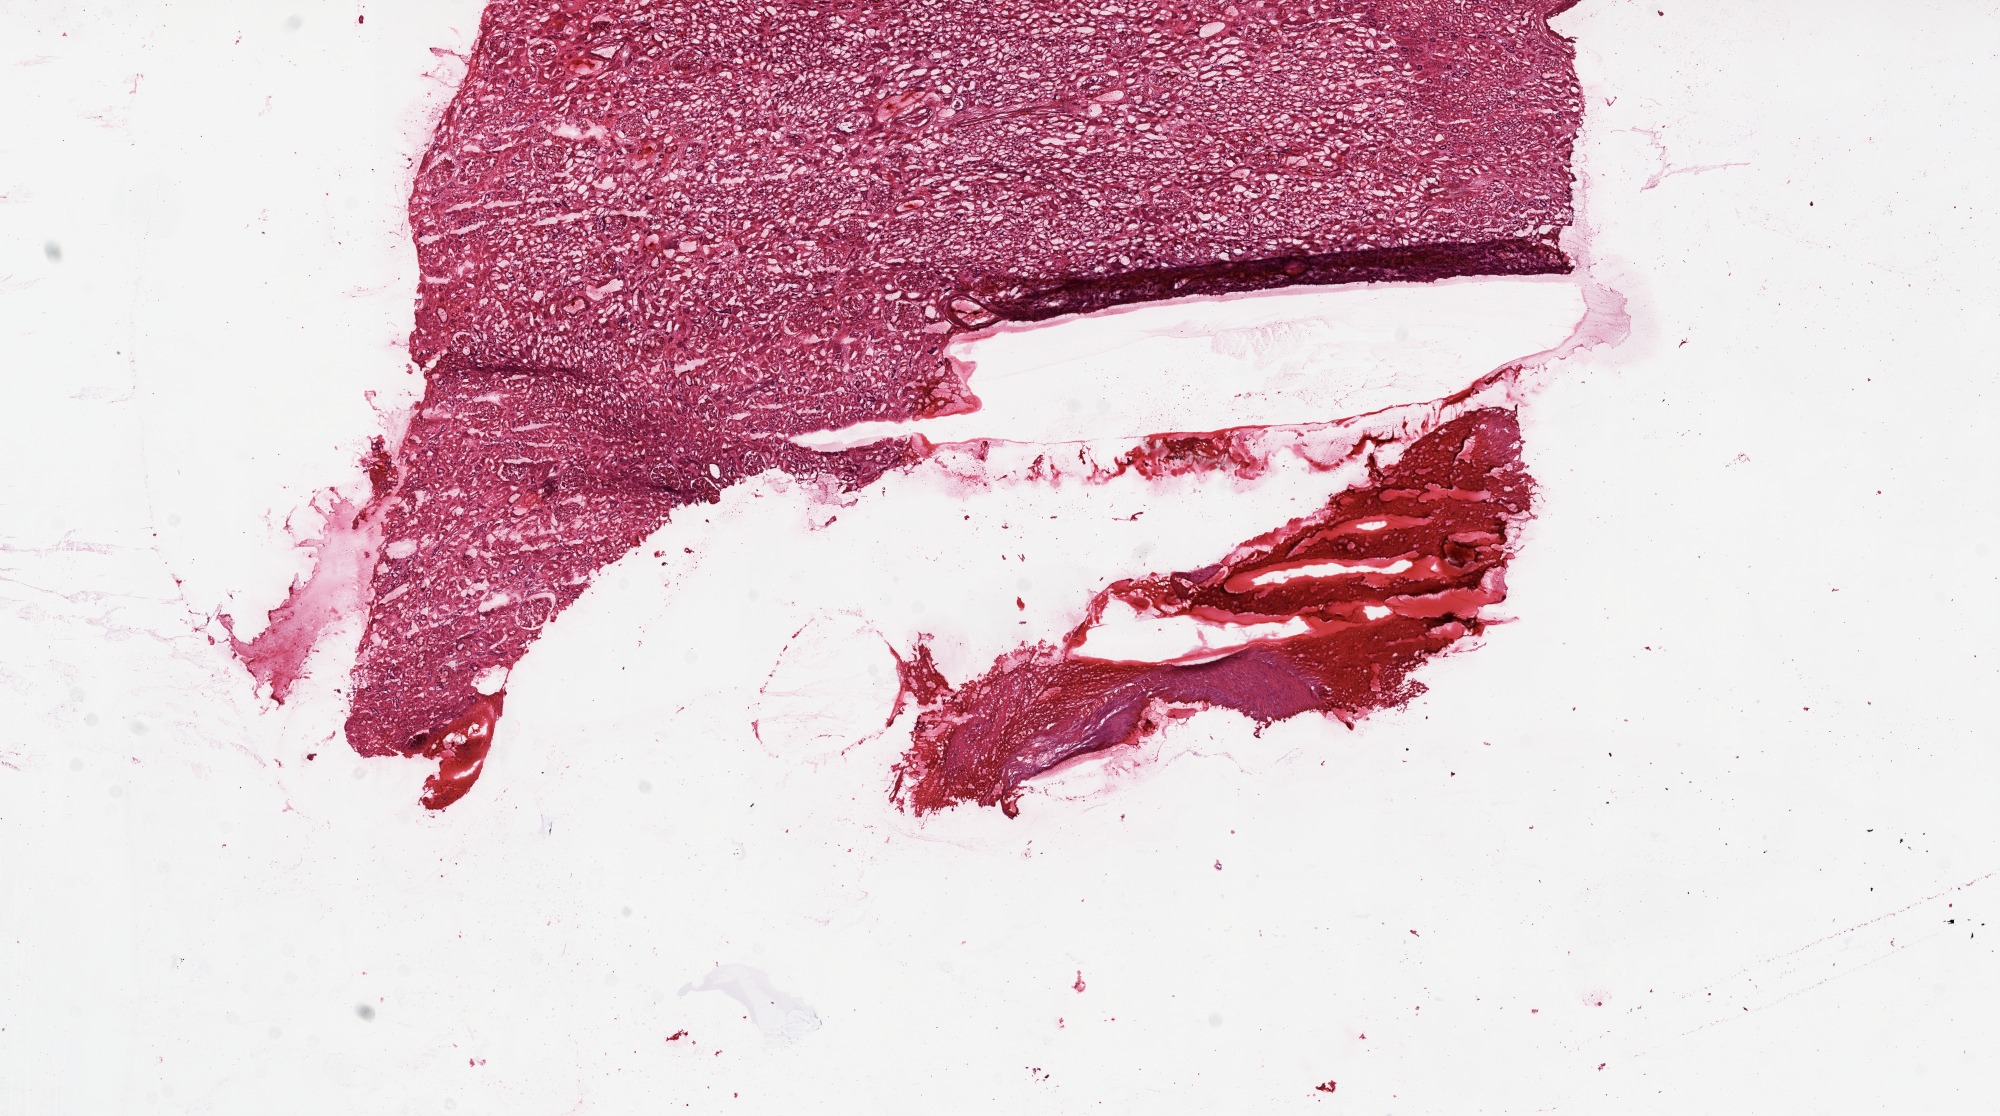
Digitized H&E-stained tissue section (whole slide) — whole scanned area (about 16.0 x 9.0 mm, slide scanned at 20x) shown as a low-resolution overview, frozen section, sample: solid tissue normal (non-tumour tissue), kidney. Patient: male, age at initial diagnosis 60 years.
This section: solid tissue normal sample (biorepository sample class). Patient diagnosis: Clear cell adenocarcinoma, NOS.